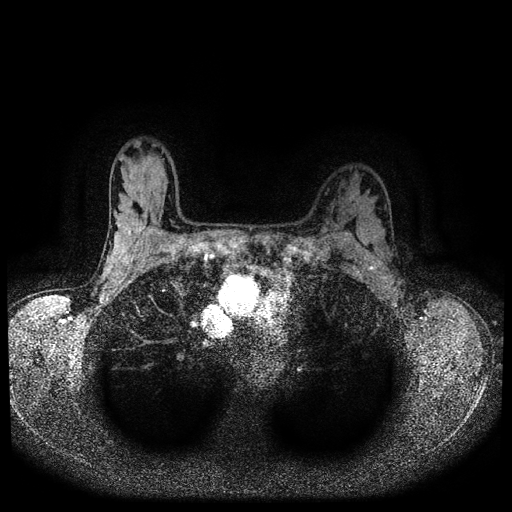
Breast MRI (dynamic contrast-enhanced, multi-phase), one axial slice. Slice 75 of 116 in the series (ordered by position). Dynamic contrast-enhanced series, time point 2 of 5 at this slice position (early post-contrast). 1.5 T. TE 2.7 ms, TR 5.4 ms. 2 mm slice thickness. 512 × 512 image matrix. Patient: female, 32 years.
Outlined on this slice (semi-automatically segmented with operator editing):
- breast lesion (labelled benign in the annotation): box from (x=345, y=187) to (x=360, y=206) px